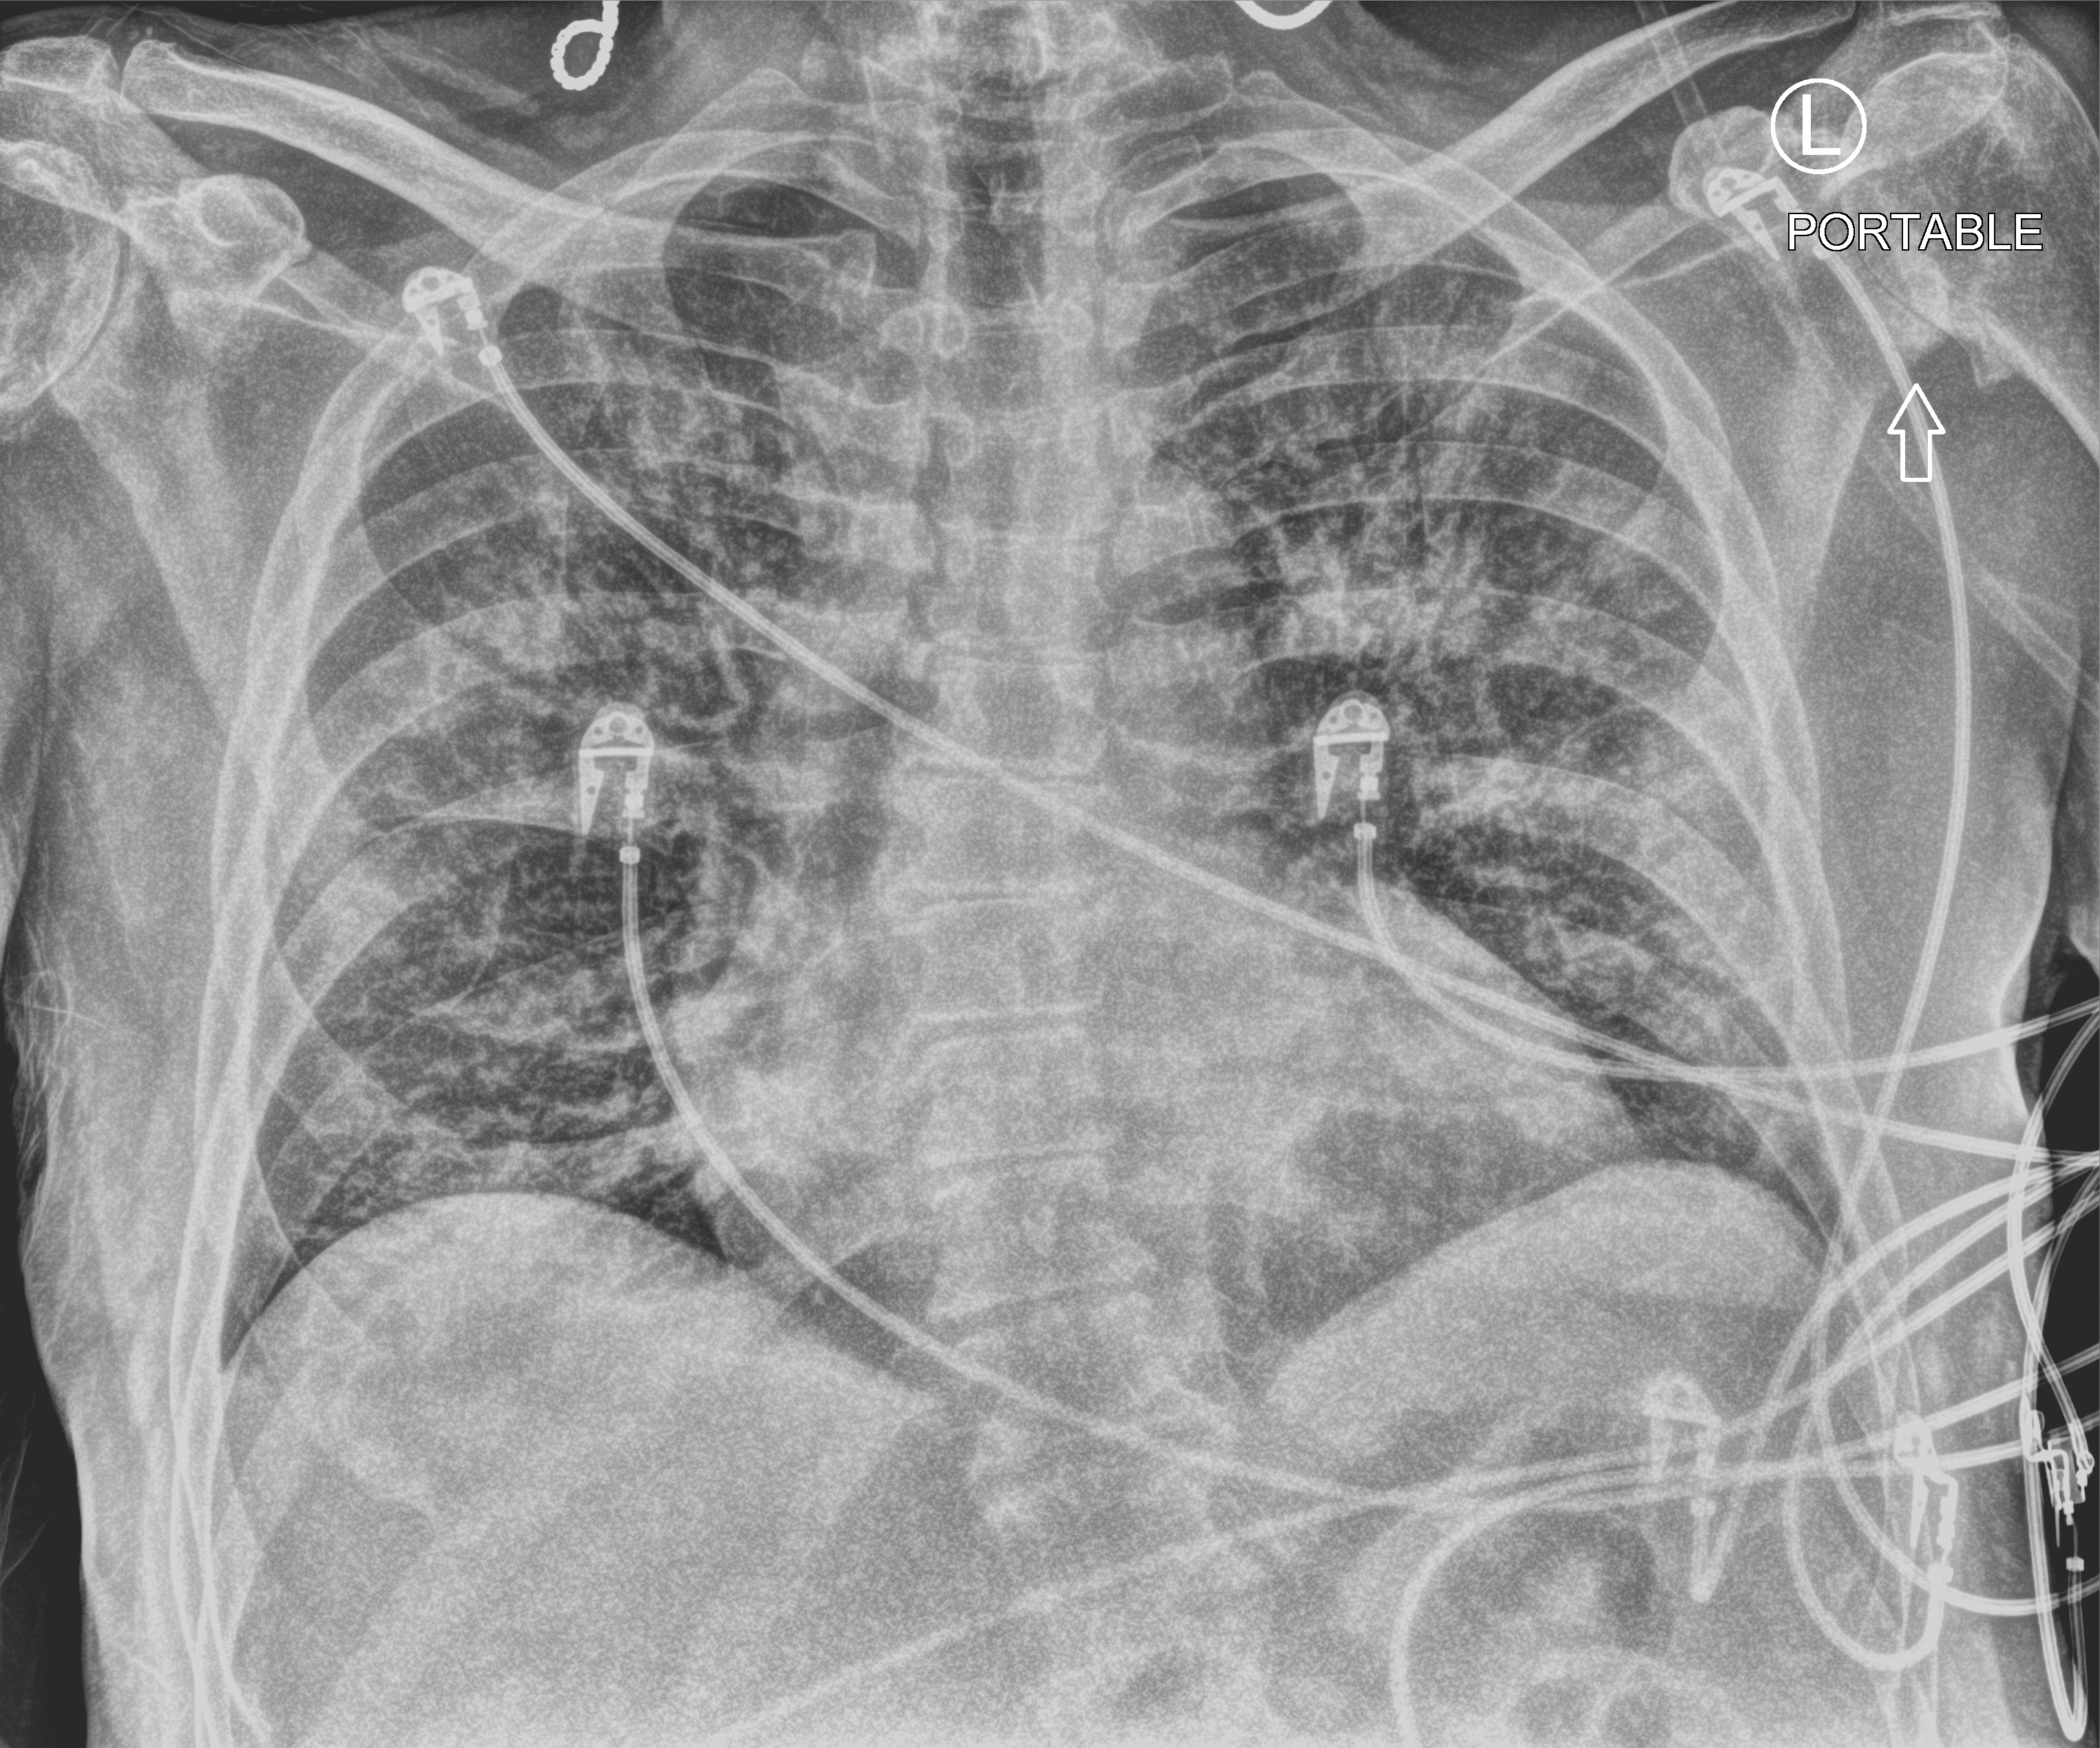
Chest X-ray (portable), anteroposterior (AP) projection. Patient hospitalised with COVID-19; male, aged 60–74 years.
From the hospital-stay record, not from the radiograph (when in the stay this image was taken is not recorded): COPD (admission record): no.